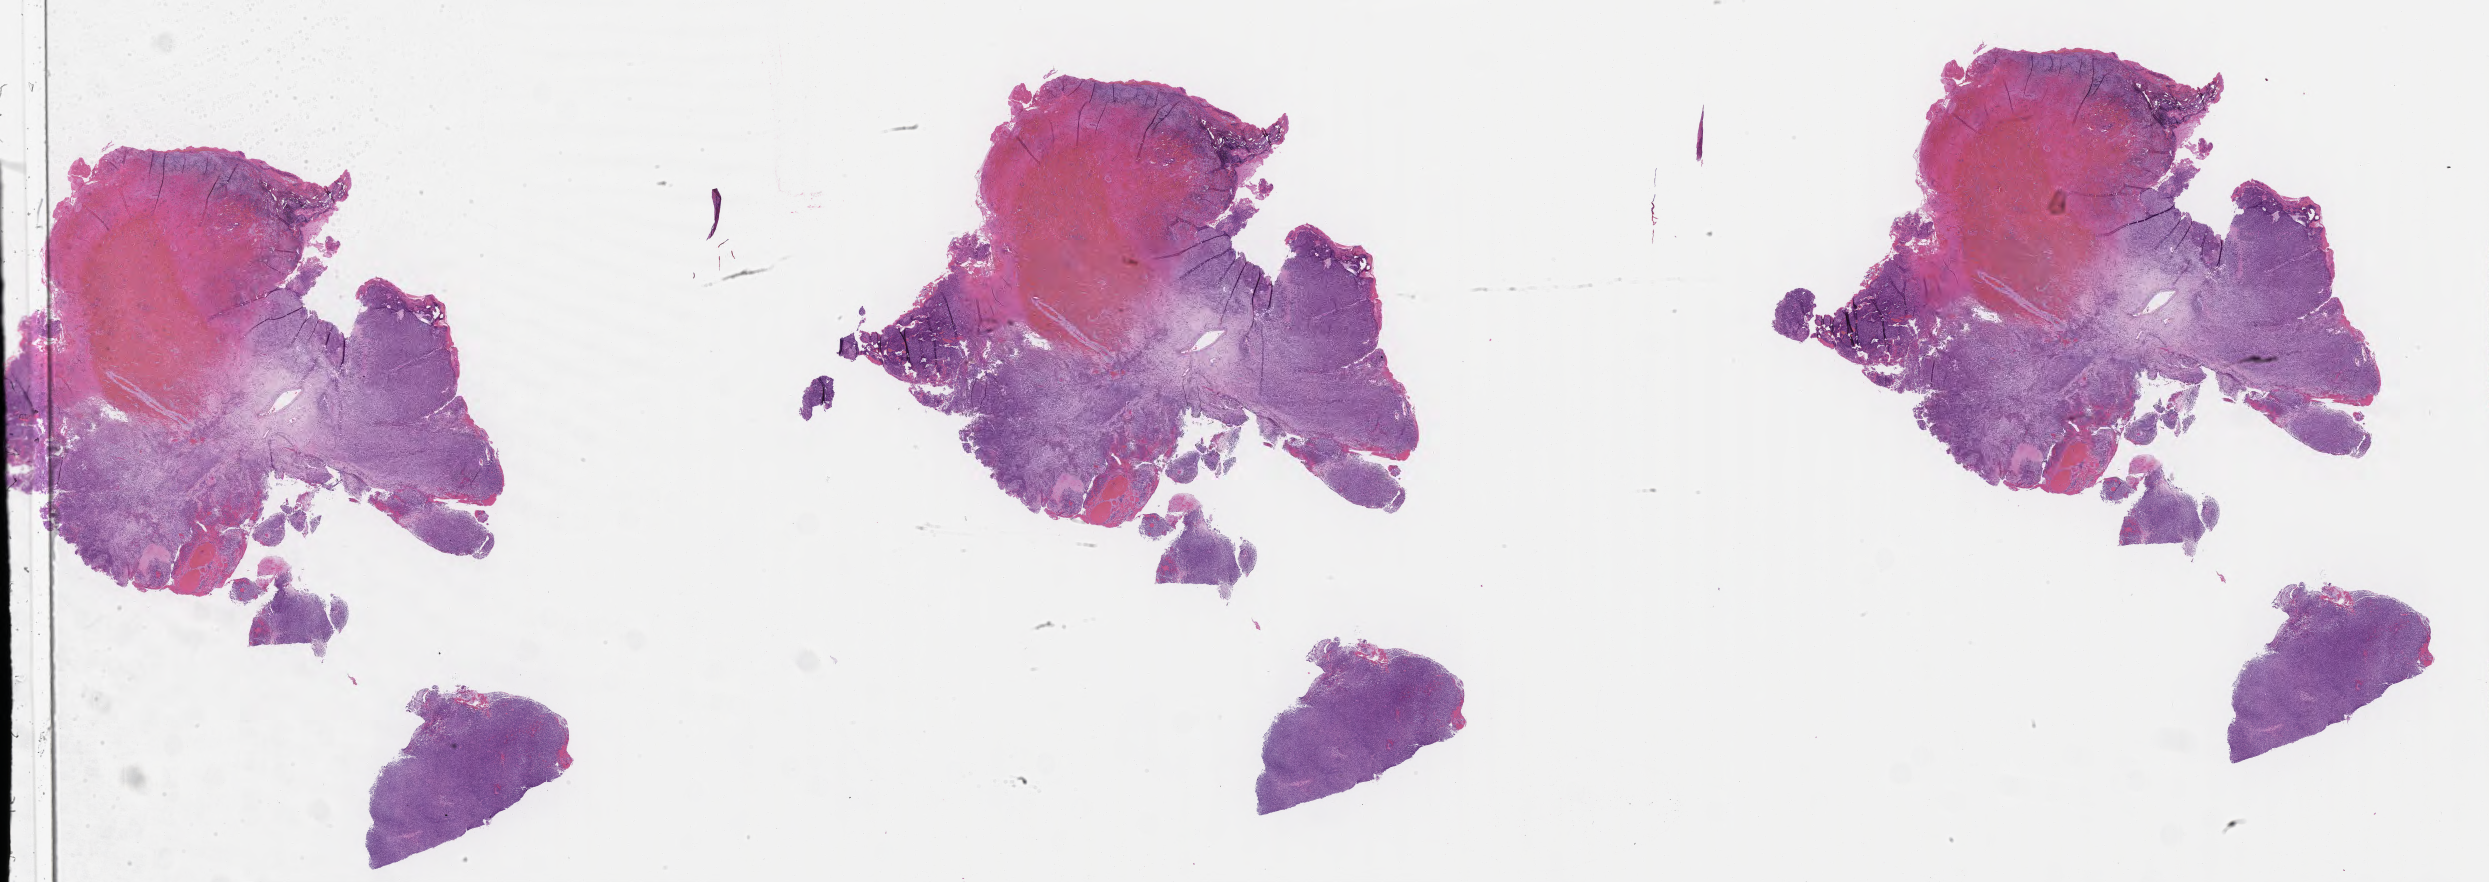
Whole-slide image, H&E stain of tumor tissue from the brain, whole scanned area (about 40.3 x 14.3 mm) shown as a low-resolution overview. FFPE section. Female patient, age 61 months (5 years 1 month).
Recorded diagnosis: Atypical teratoid/rhabdoid tumor.